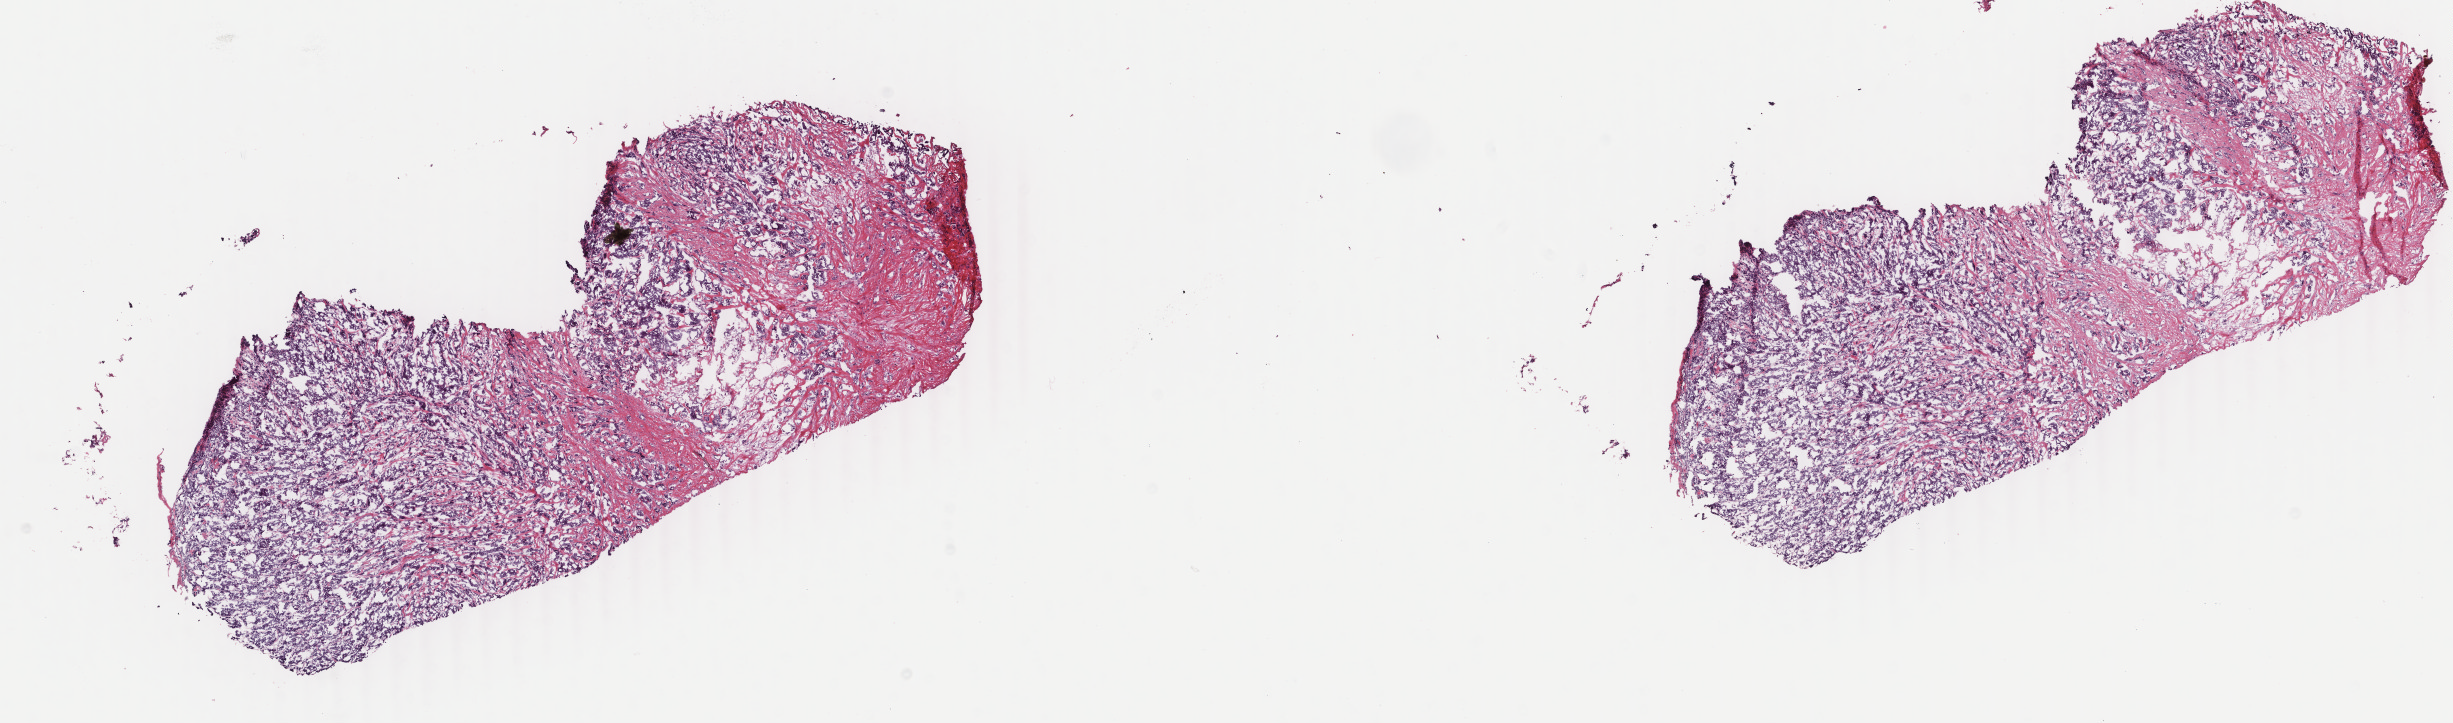
H&E-stained whole-slide image, a low-resolution overview of the entire scanned area, about 19.5 x 5.8 mm, frozen section from the bottom of the tissue portion, primary tumour sample from the breast. Female, age 55 years at initial diagnosis. Composition of this section per pathologist review: tumour cells 80%, tumour nuclei 80%.
Histologic diagnosis: Infiltrating duct carcinoma, NOS.